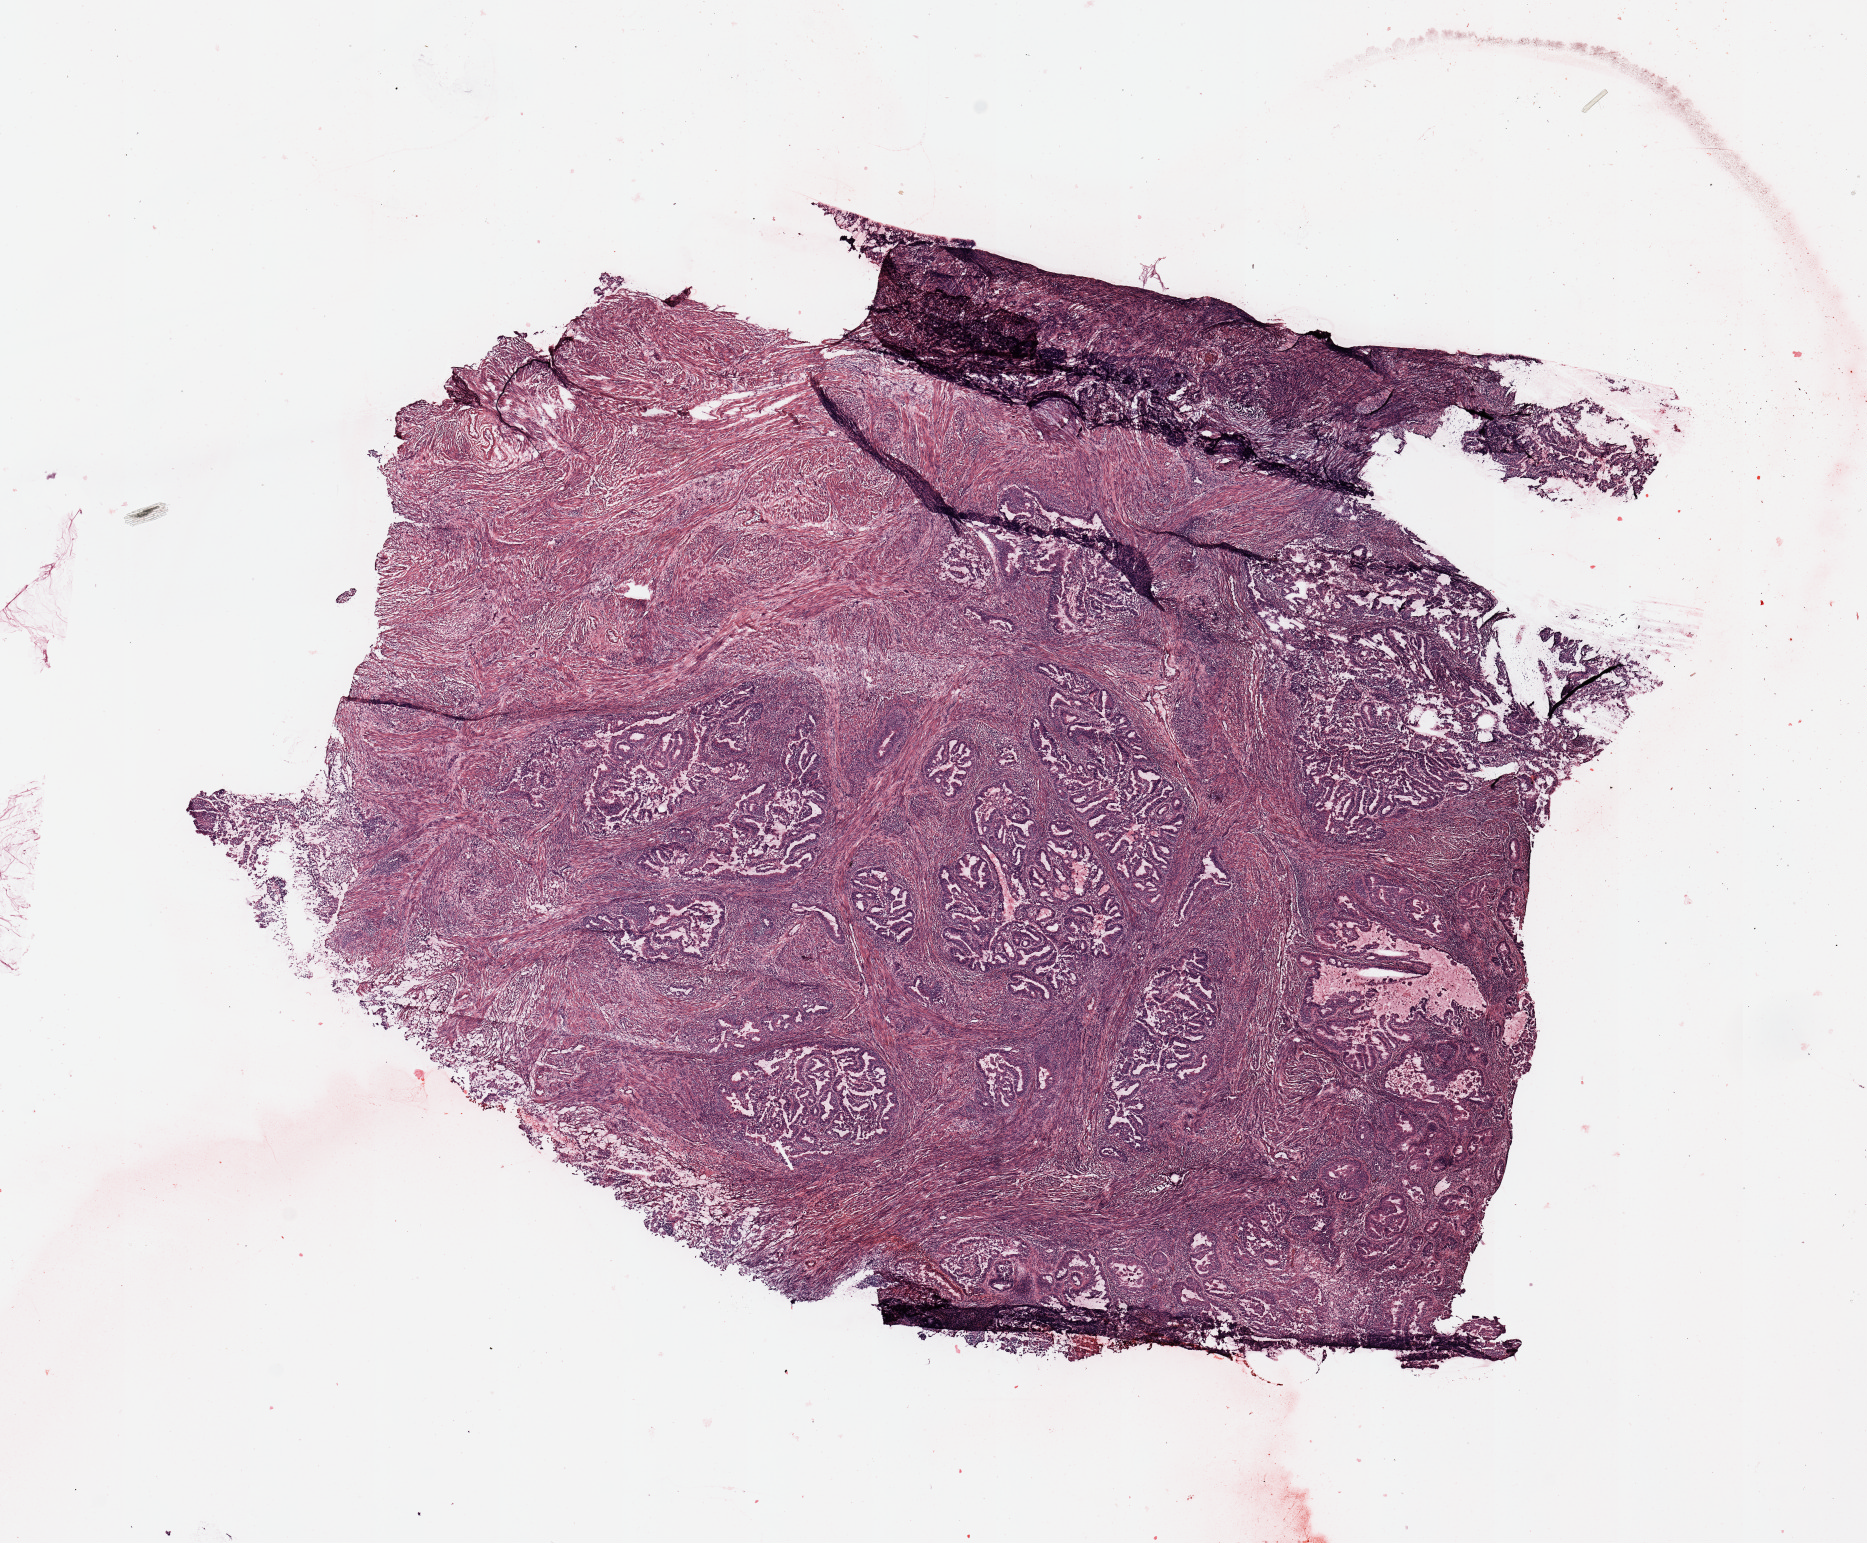
Digitized H&E tissue section (whole slide), shown as a low-resolution overview of the whole scanned area (about 14.8 x 12.2 mm, slide scanned at 20x). Tumour tissue sample, uterus. 66-year-old female patient. Histologic grade: G2 (moderately differentiated).
* diagnosis: Endometrioid adenocarcinoma, NOS
* AJCC pathologic stage: II